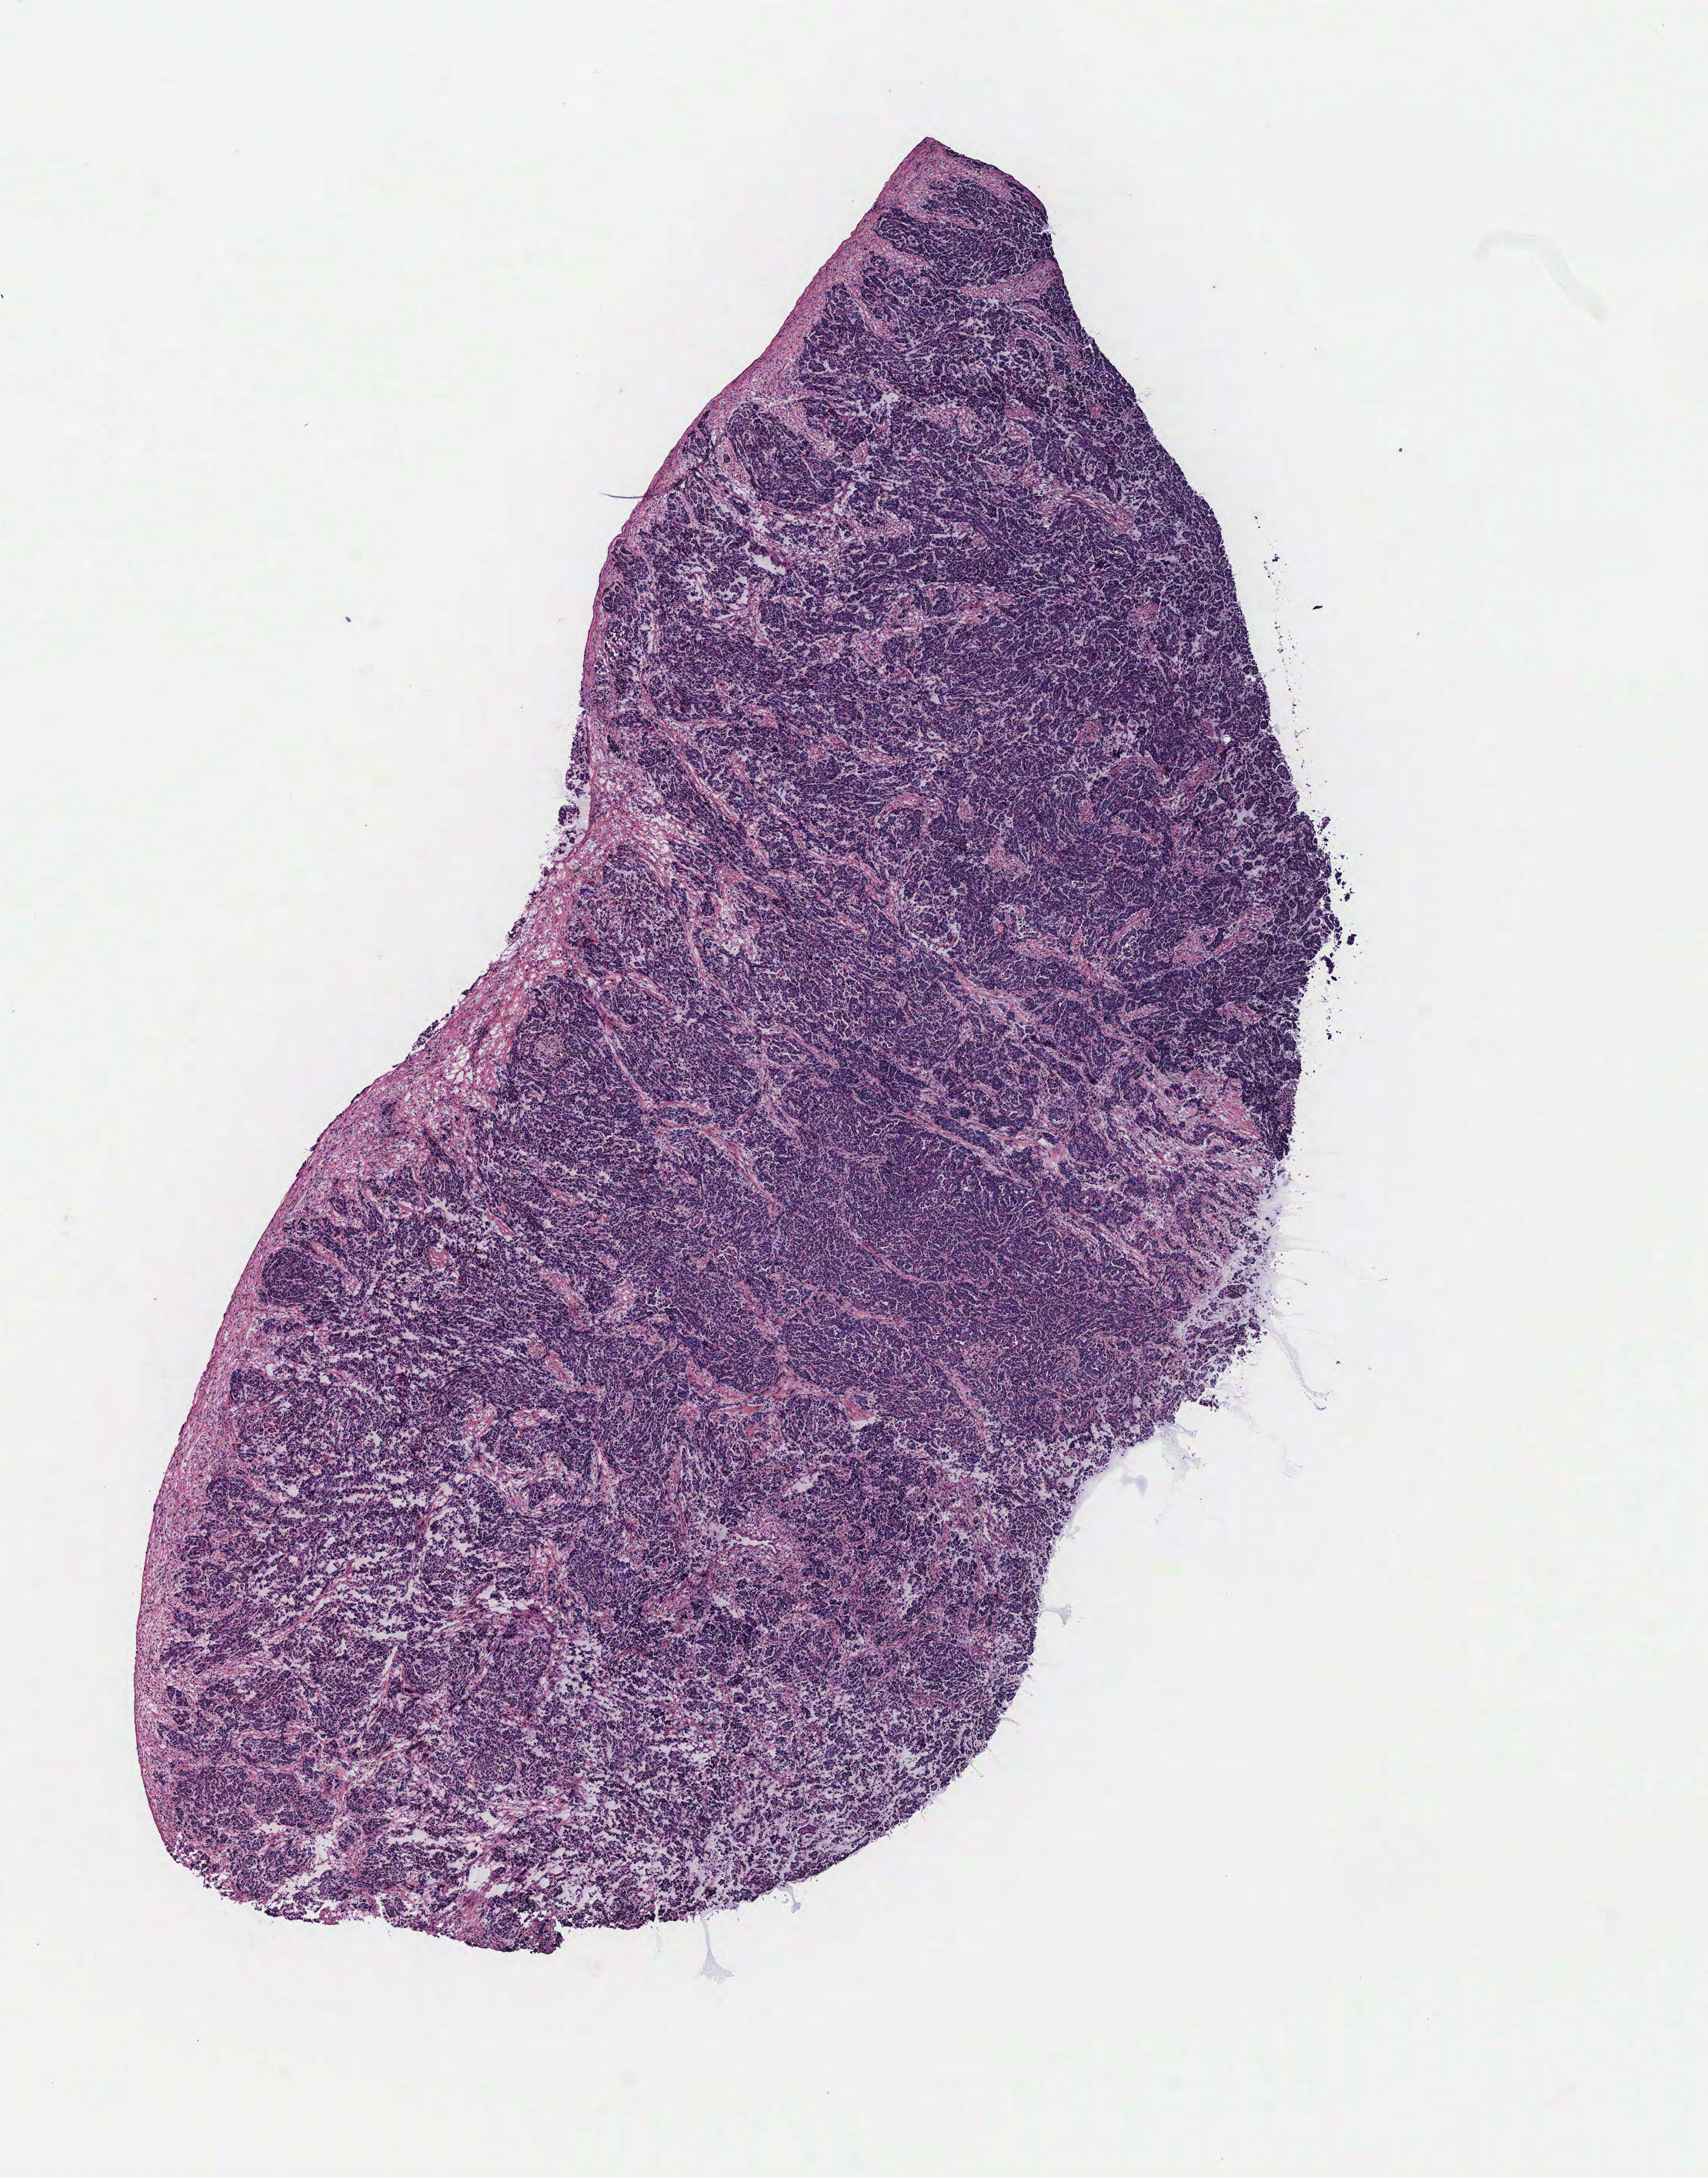
Digitized H&E tissue section (whole slide) — a low-resolution overview of the entire scanned area, about 8.9 x 11.3 mm (slide scanned at 40x), tumour tissue sample, ovary. 77-year-old female patient.
Primary tumour site (as recorded): ovary. Histologic diagnosis: Serous adenocarcinoma, NOS.